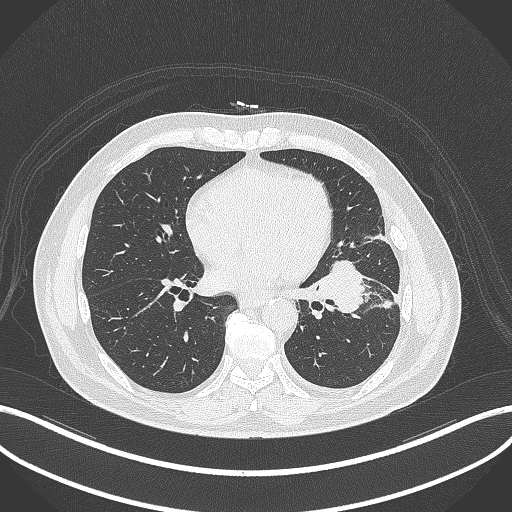
Chest CT, one axial slice. Position 153 of 230 along the scan axis. 120 kVp. Lung window (W 1500 / L -600 HU). 1 mm slice thickness. 512 × 512 image matrix, field of view 400 × 400 mm. Patient: male, 68 years. Case-level facts recorded for this patient, not image findings: clinical TNM (as recorded): T2b N0 M0.
Outlined on this slice (rectangle marked by the reading radiologist):
- lung tumour (recorded histology: squamous cell carcinoma): bounding box (x1, y1, x2, y2) in pixels: (314, 257, 369, 321)